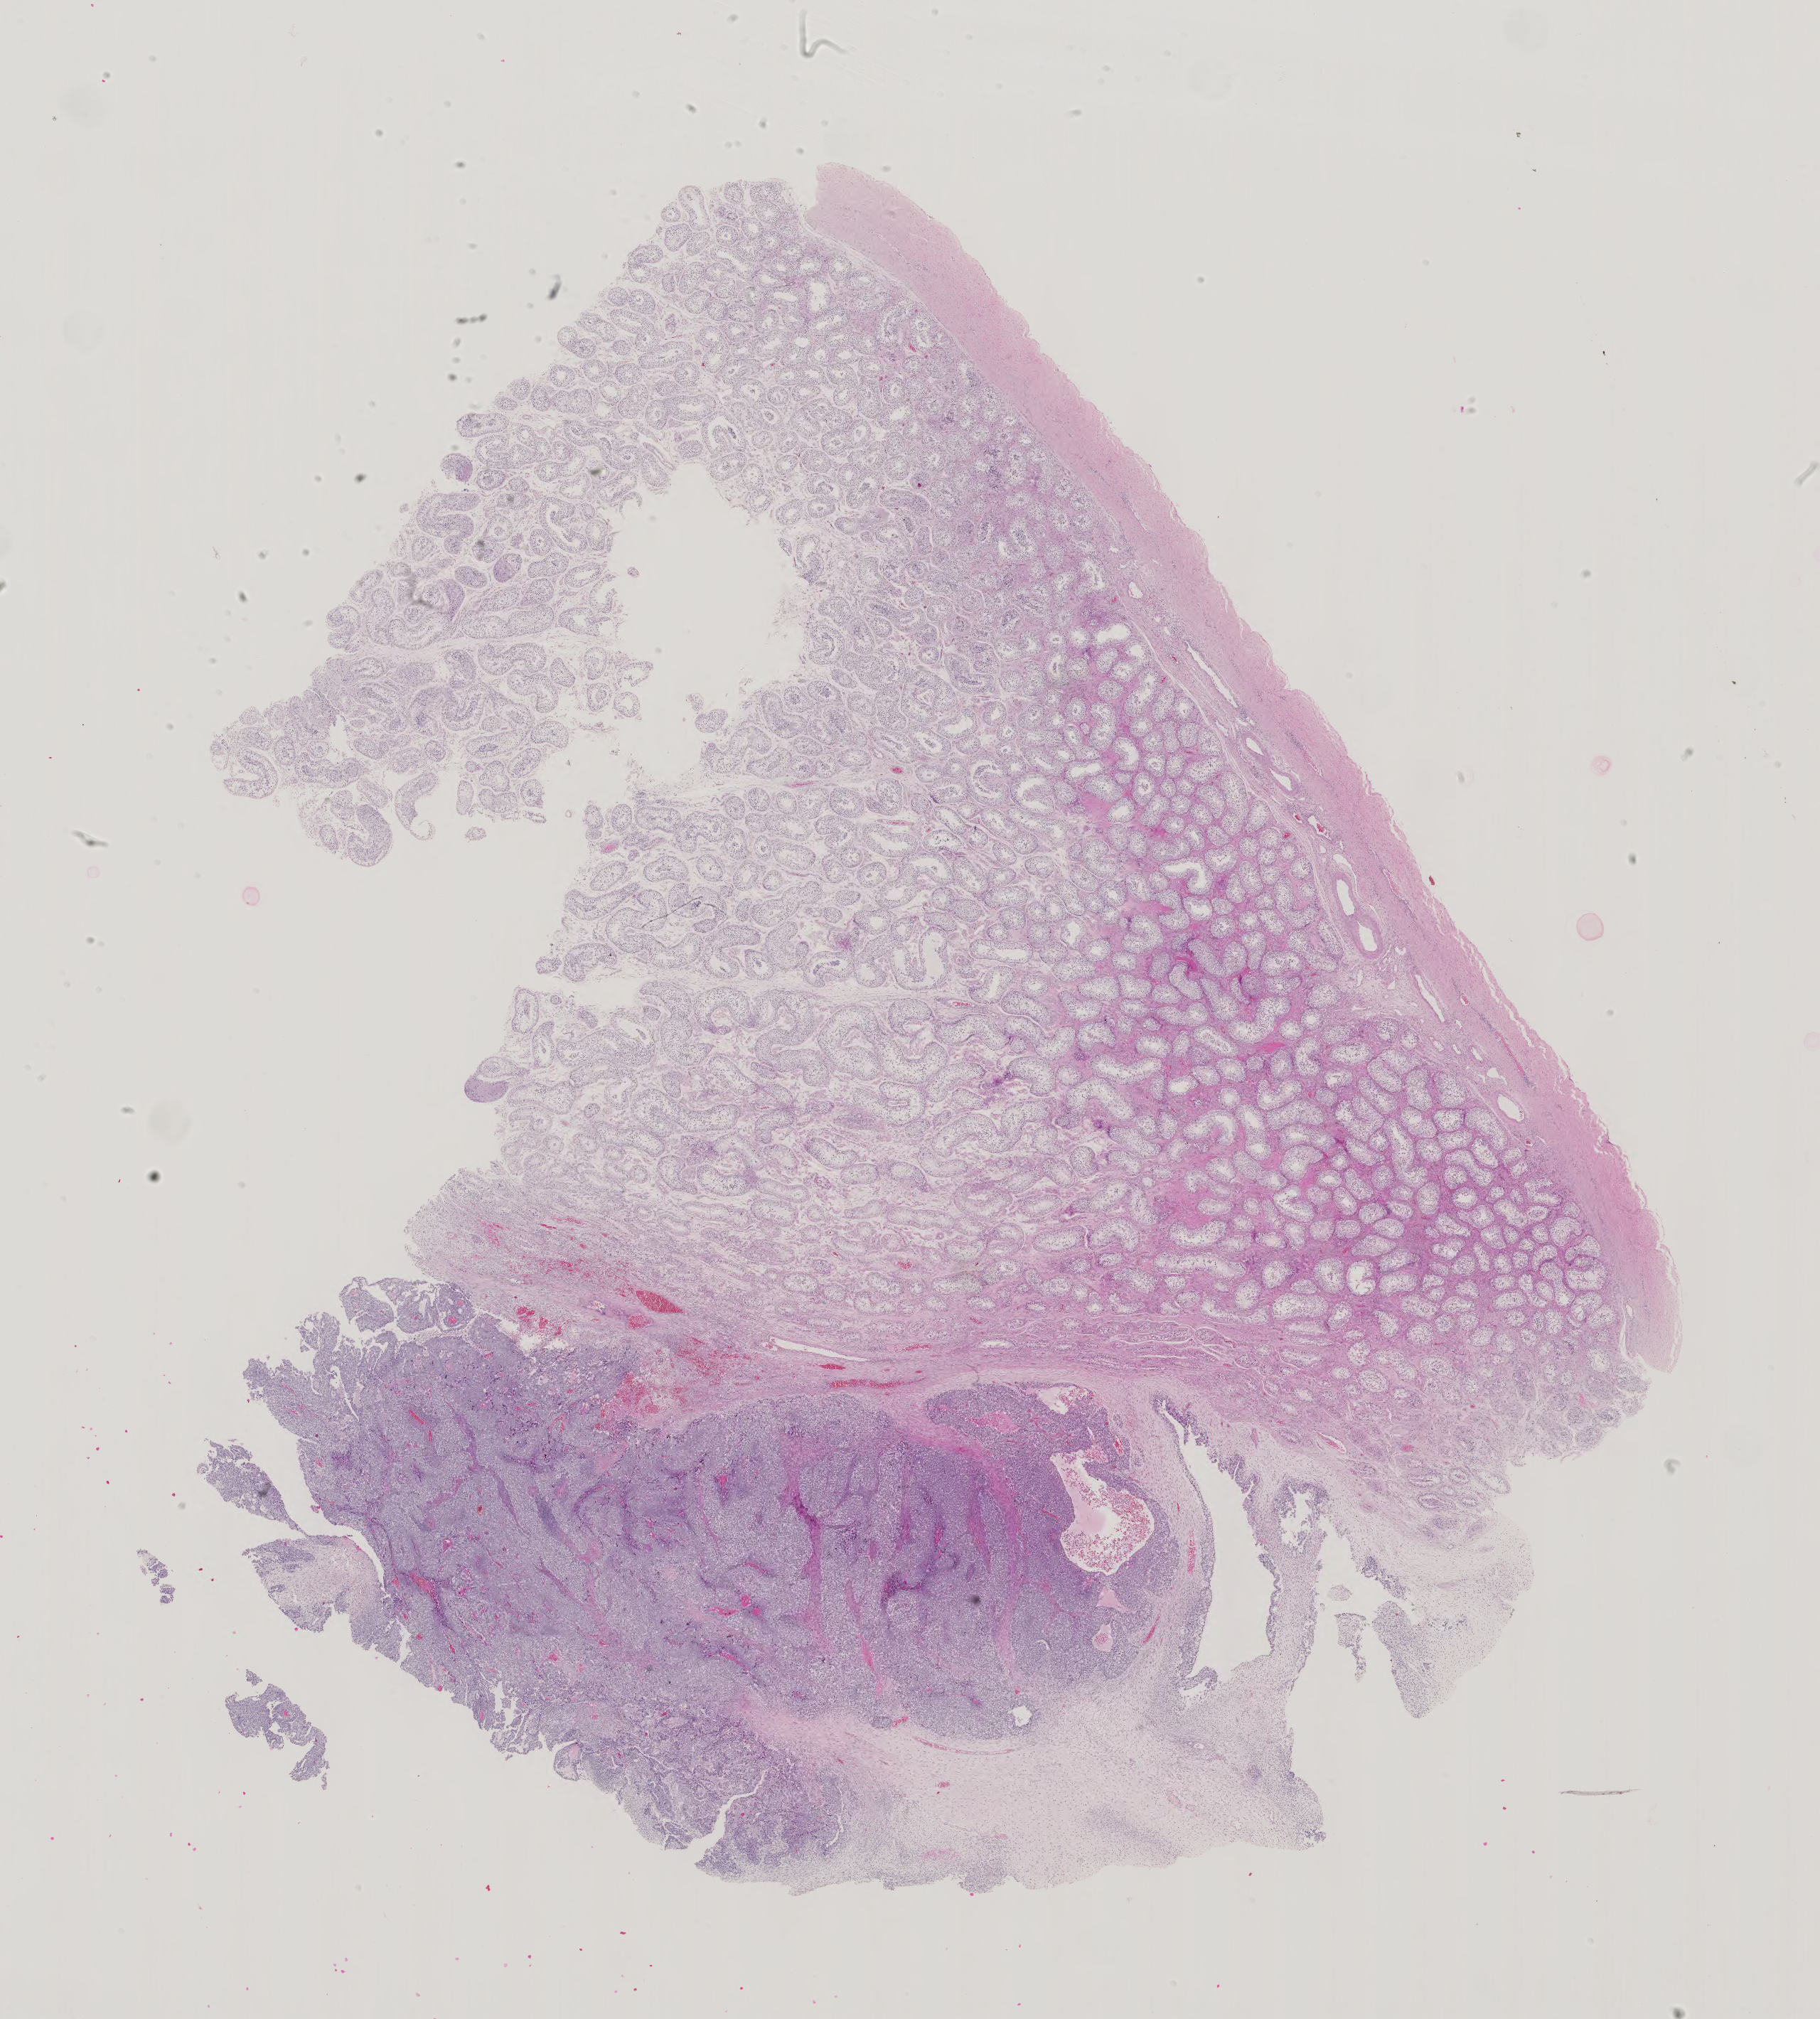
Whole-slide histology image, H&E, a low-resolution overview of the entire scanned area, about 18.7 x 20.7 mm. Male patient.
• specimen: formalin-fixed paraffin-embedded (FFPE) diagnostic section; testis, primary tumour sample